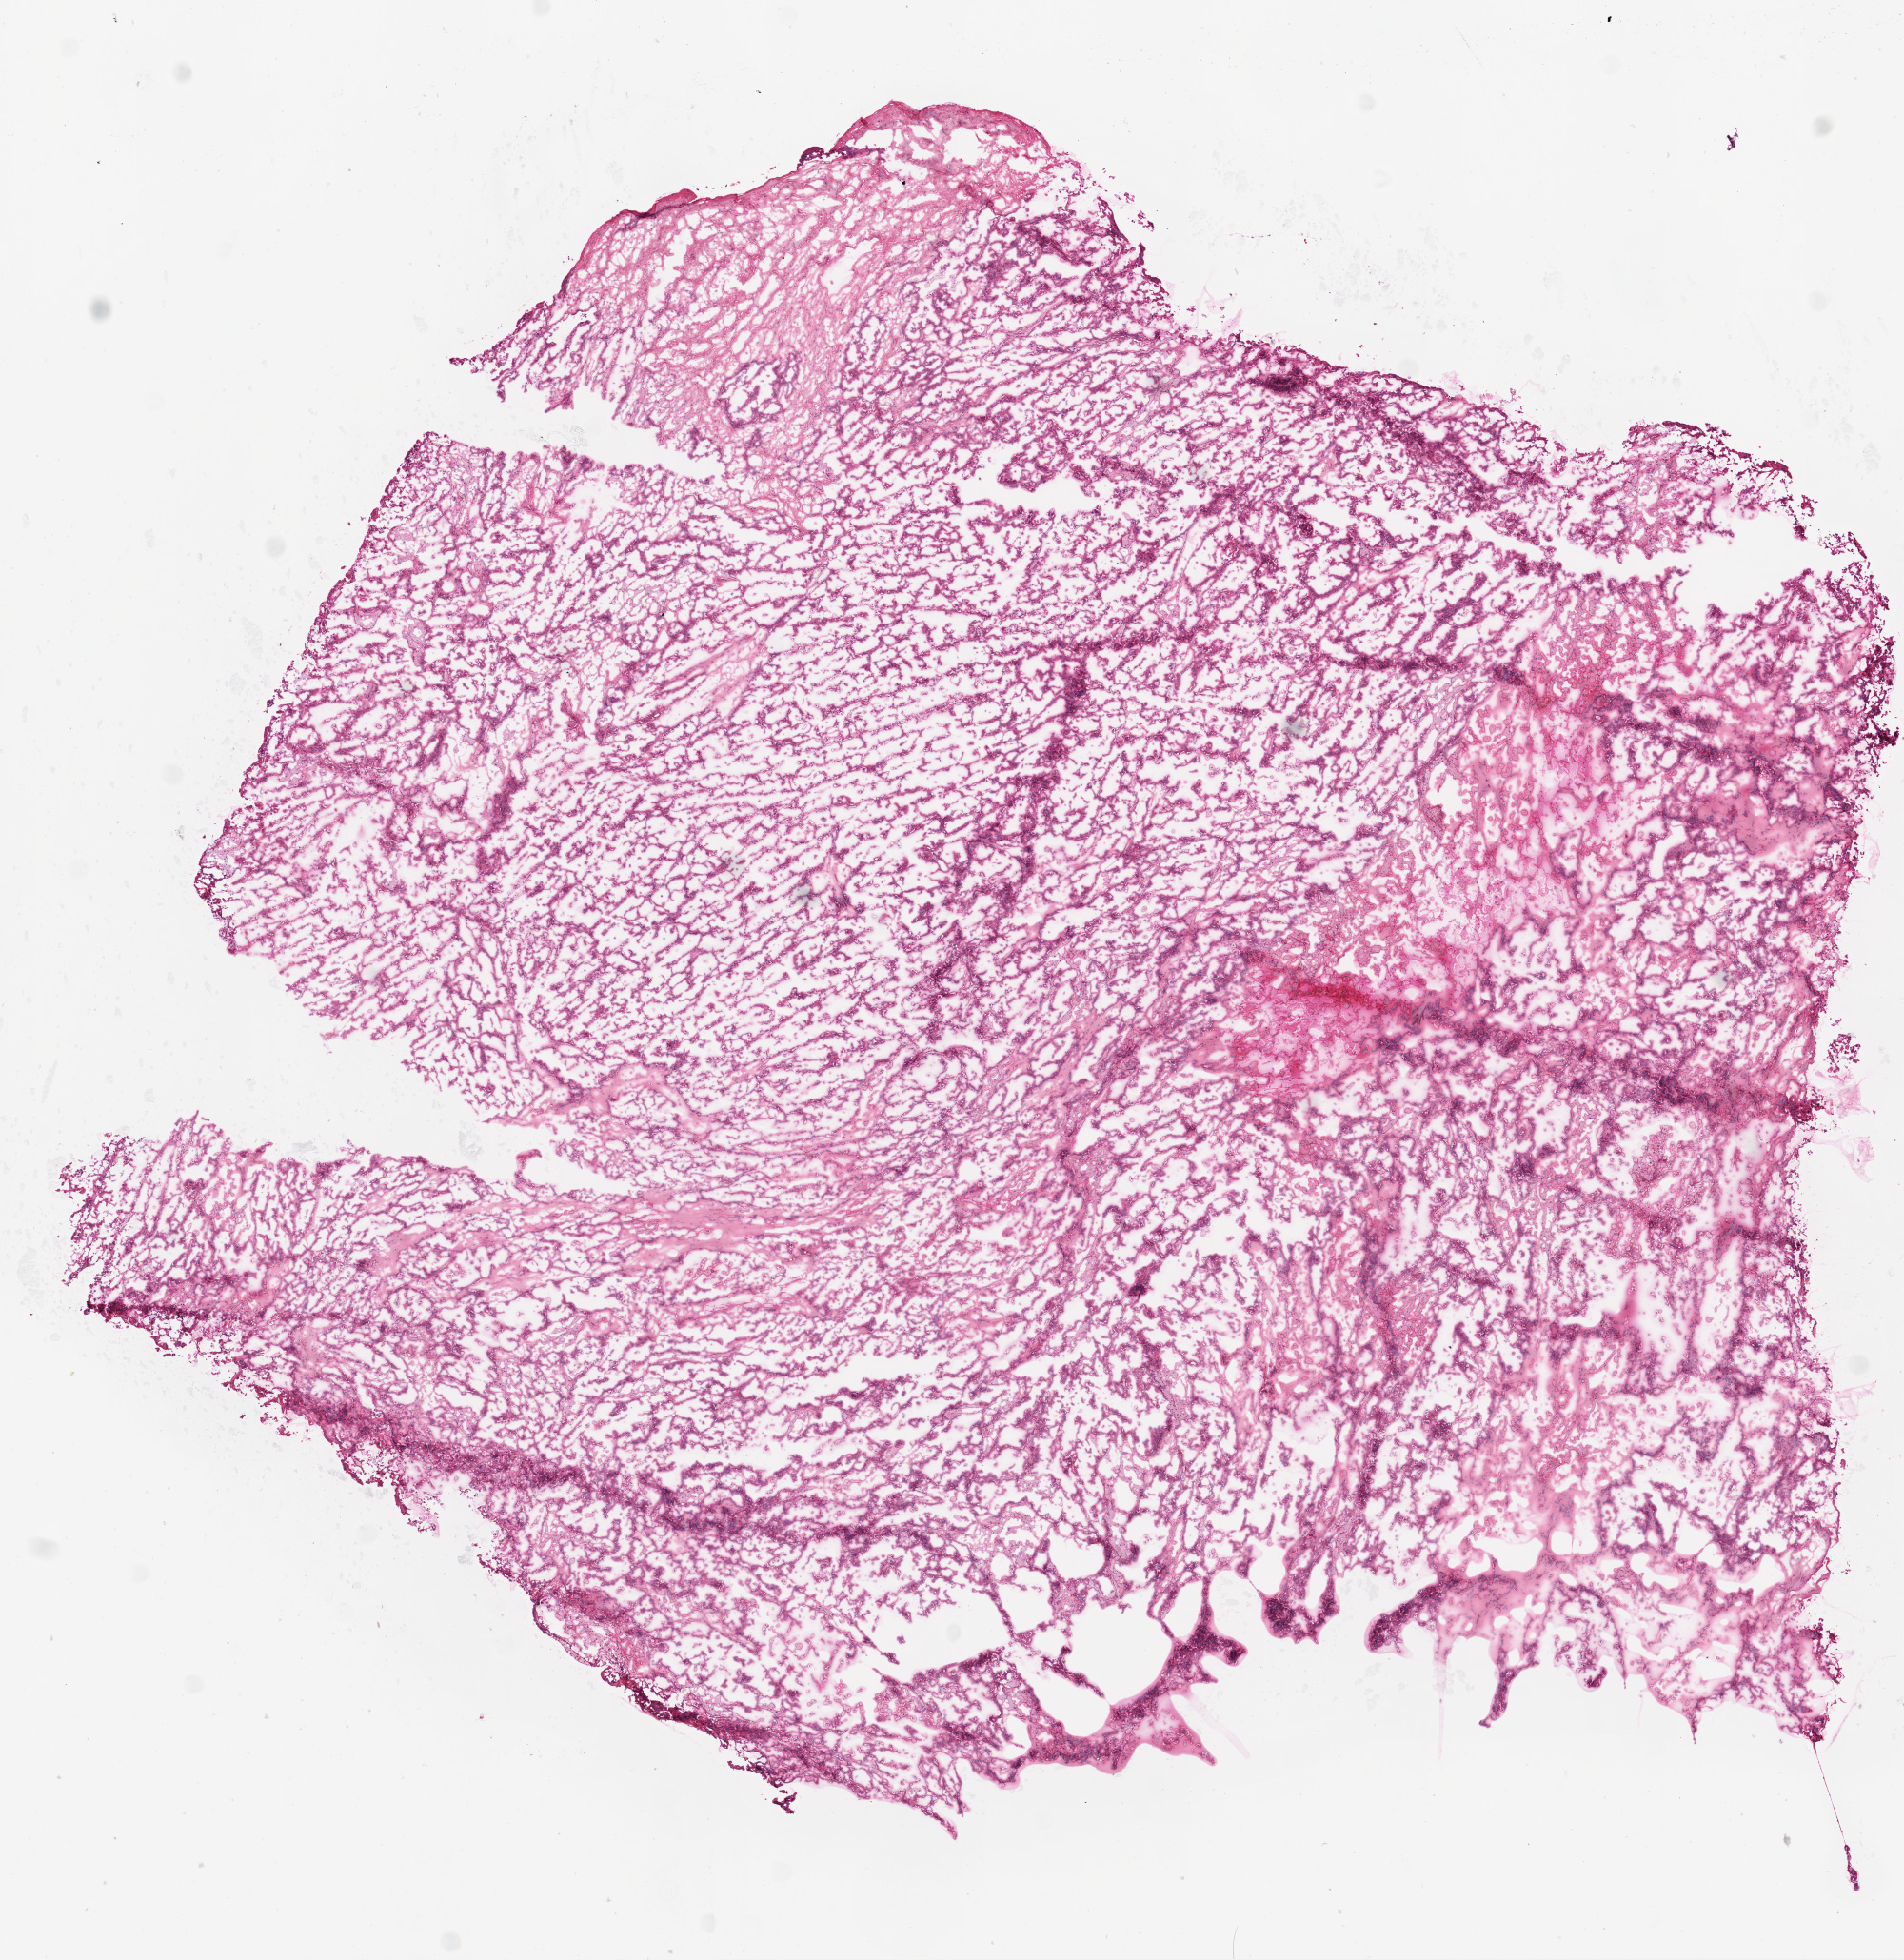
H&E-stained whole-slide image, low-resolution overview of the scanned area, about 8.0 x 8.3 mm; frozen section; kidney, primary tumour sample. Patient: male, age at initial diagnosis 55 years. Composition of this section per pathologist review: tumour cells 95%, tumour nuclei 80%, normal cells 0%, stromal cells 5%, necrosis 0%.
Diagnosis: Papillary adenocarcinoma, NOS. AJCC pathologic stage: II (6th edition). Laterality: left. Lymph nodes positive (case pathology): 0 of 33 examined.